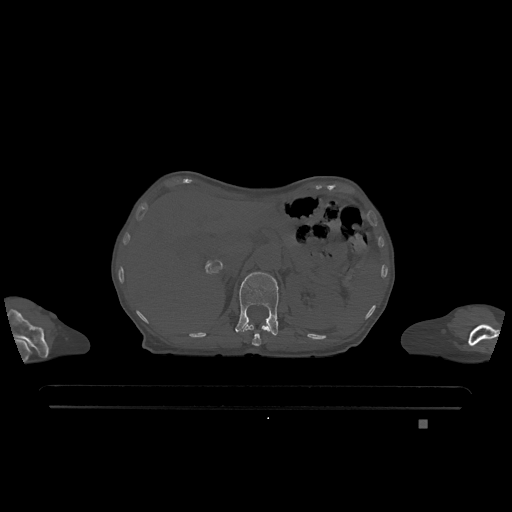
CT including the spine, one axial slice; position 492 of 1317 along the scan axis; bone window (W 1800 / L 400 HU); 512 × 512 image matrix. Female patient, age 74 years. From the clinical record (not read from this slice): primary cancer: lung.
Outlined on this slice (semi-automatically segmented with operator editing):
- L1 vertebra: bounding box (x1, y1, x2, y2) in pixels: (236, 272, 279, 336)
- T12 vertebra: (242, 324, 270, 346)